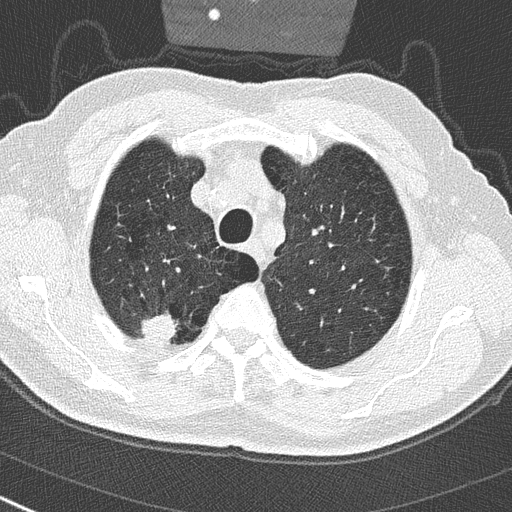
Low-dose screening chest CT, axial slice. First (baseline) screen. Lung window (W 1500 / L -600 HU). Male participant, aged 65 years at enrolment.
• Lesion marked by an expert reader, bounding box [x1, y1, x2, y2] px = [135, 304, 185, 352].
• Reader record for this screening exam (exam-level; its link to the box is not recorded): non-calcified nodule or mass ≥4 mm, right upper lobe, 24 × 19 mm, spiculated (stellate) margins, soft tissue attenuation.
• Official screen result: positive, change unspecified: nodule(s) >= 4 mm or enlarging nodule(s), mass(es), or other non-specific abnormalities suspicious for lung cancer.
• Later outcome: lung cancer diagnosed 32 days after this screen — non-small cell carcinoma, right upper lobe, poorly differentiated (G3), stage IA (AJCC 6th edition), 29 mm at pathology.